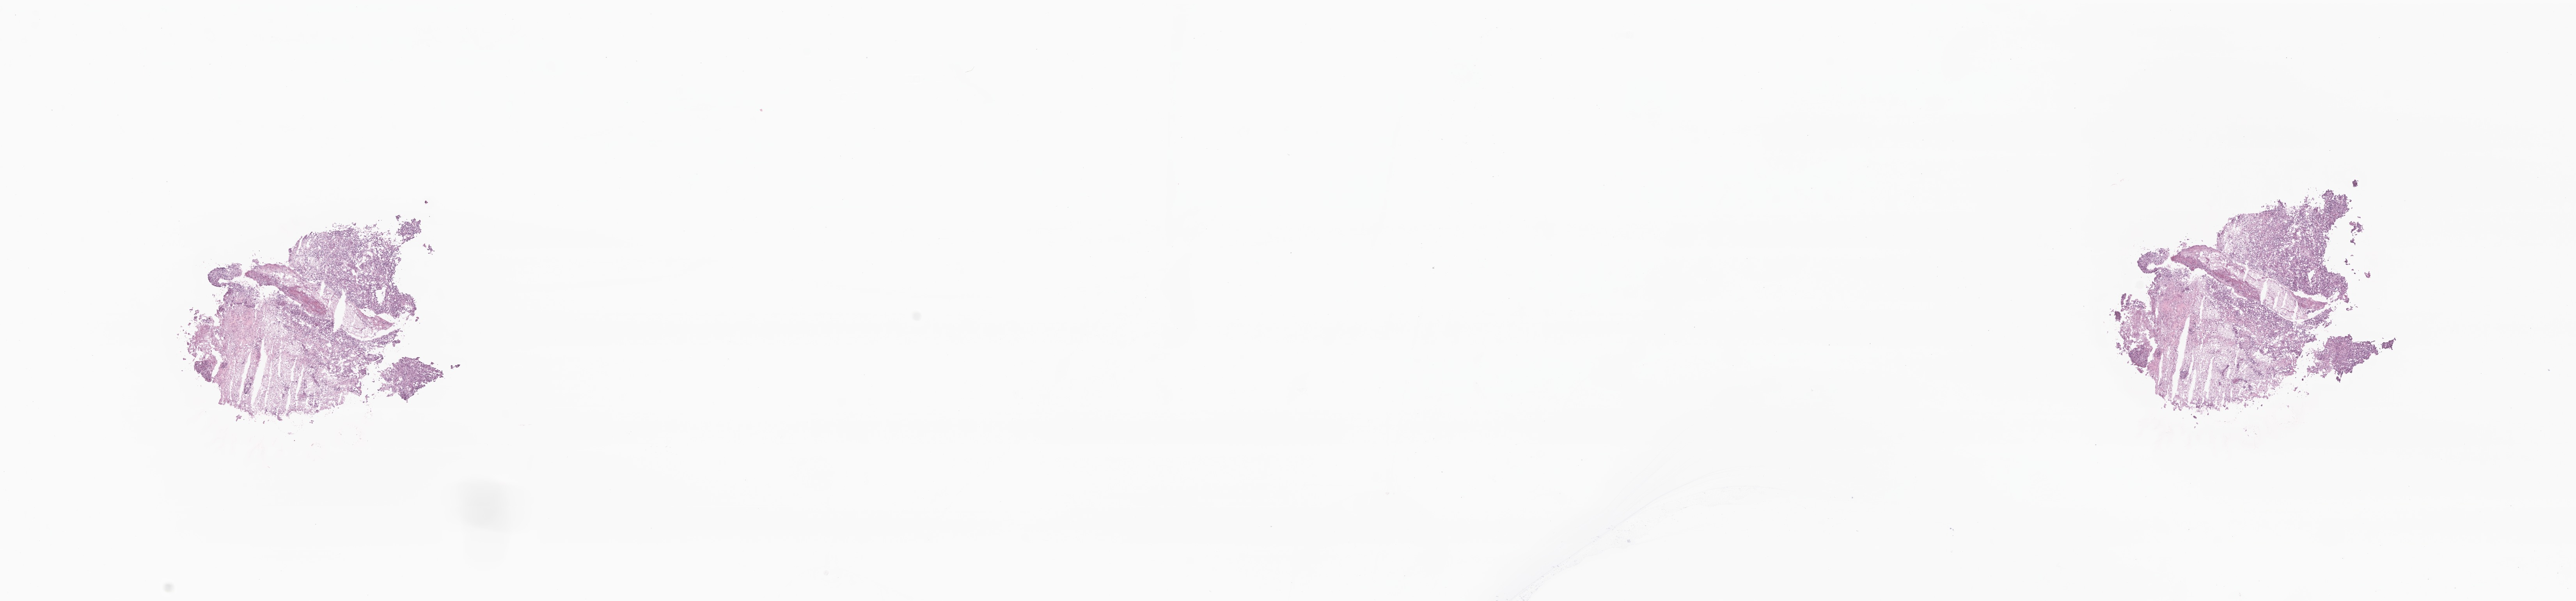
Haematoxylin and eosin whole-slide image of tumor tissue from the brain, shown as a low-resolution overview of the whole scanned area (about 27.8 x 6.5 mm); frozen section (OCT-embedded). Patient female; age 183 months.
Diagnosis (ICD-O-3 morphology term): Ependymoma, anaplastic.